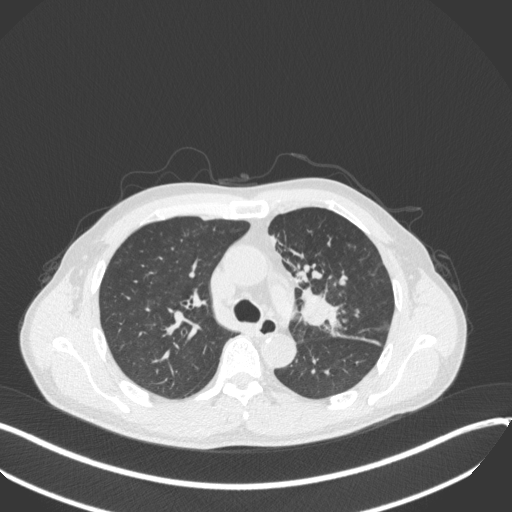
Chest CT, one axial slice. Position 229 of 411 along the scan axis. Reconstruction kernel B31f. 120 kVp. Lung window (W 1500 / L -600 HU). 512 × 512 image matrix, field of view 400 × 400 mm. Patient: male, 56 years. Case-level facts recorded for this patient, not image findings: clinical TNM (as recorded): T2a N0 M0.
Structures marked on this image (rectangle marked by the reading radiologist):
- lung tumour (recorded histology: squamous cell carcinoma): box from (x=294, y=280) to (x=347, y=336) px